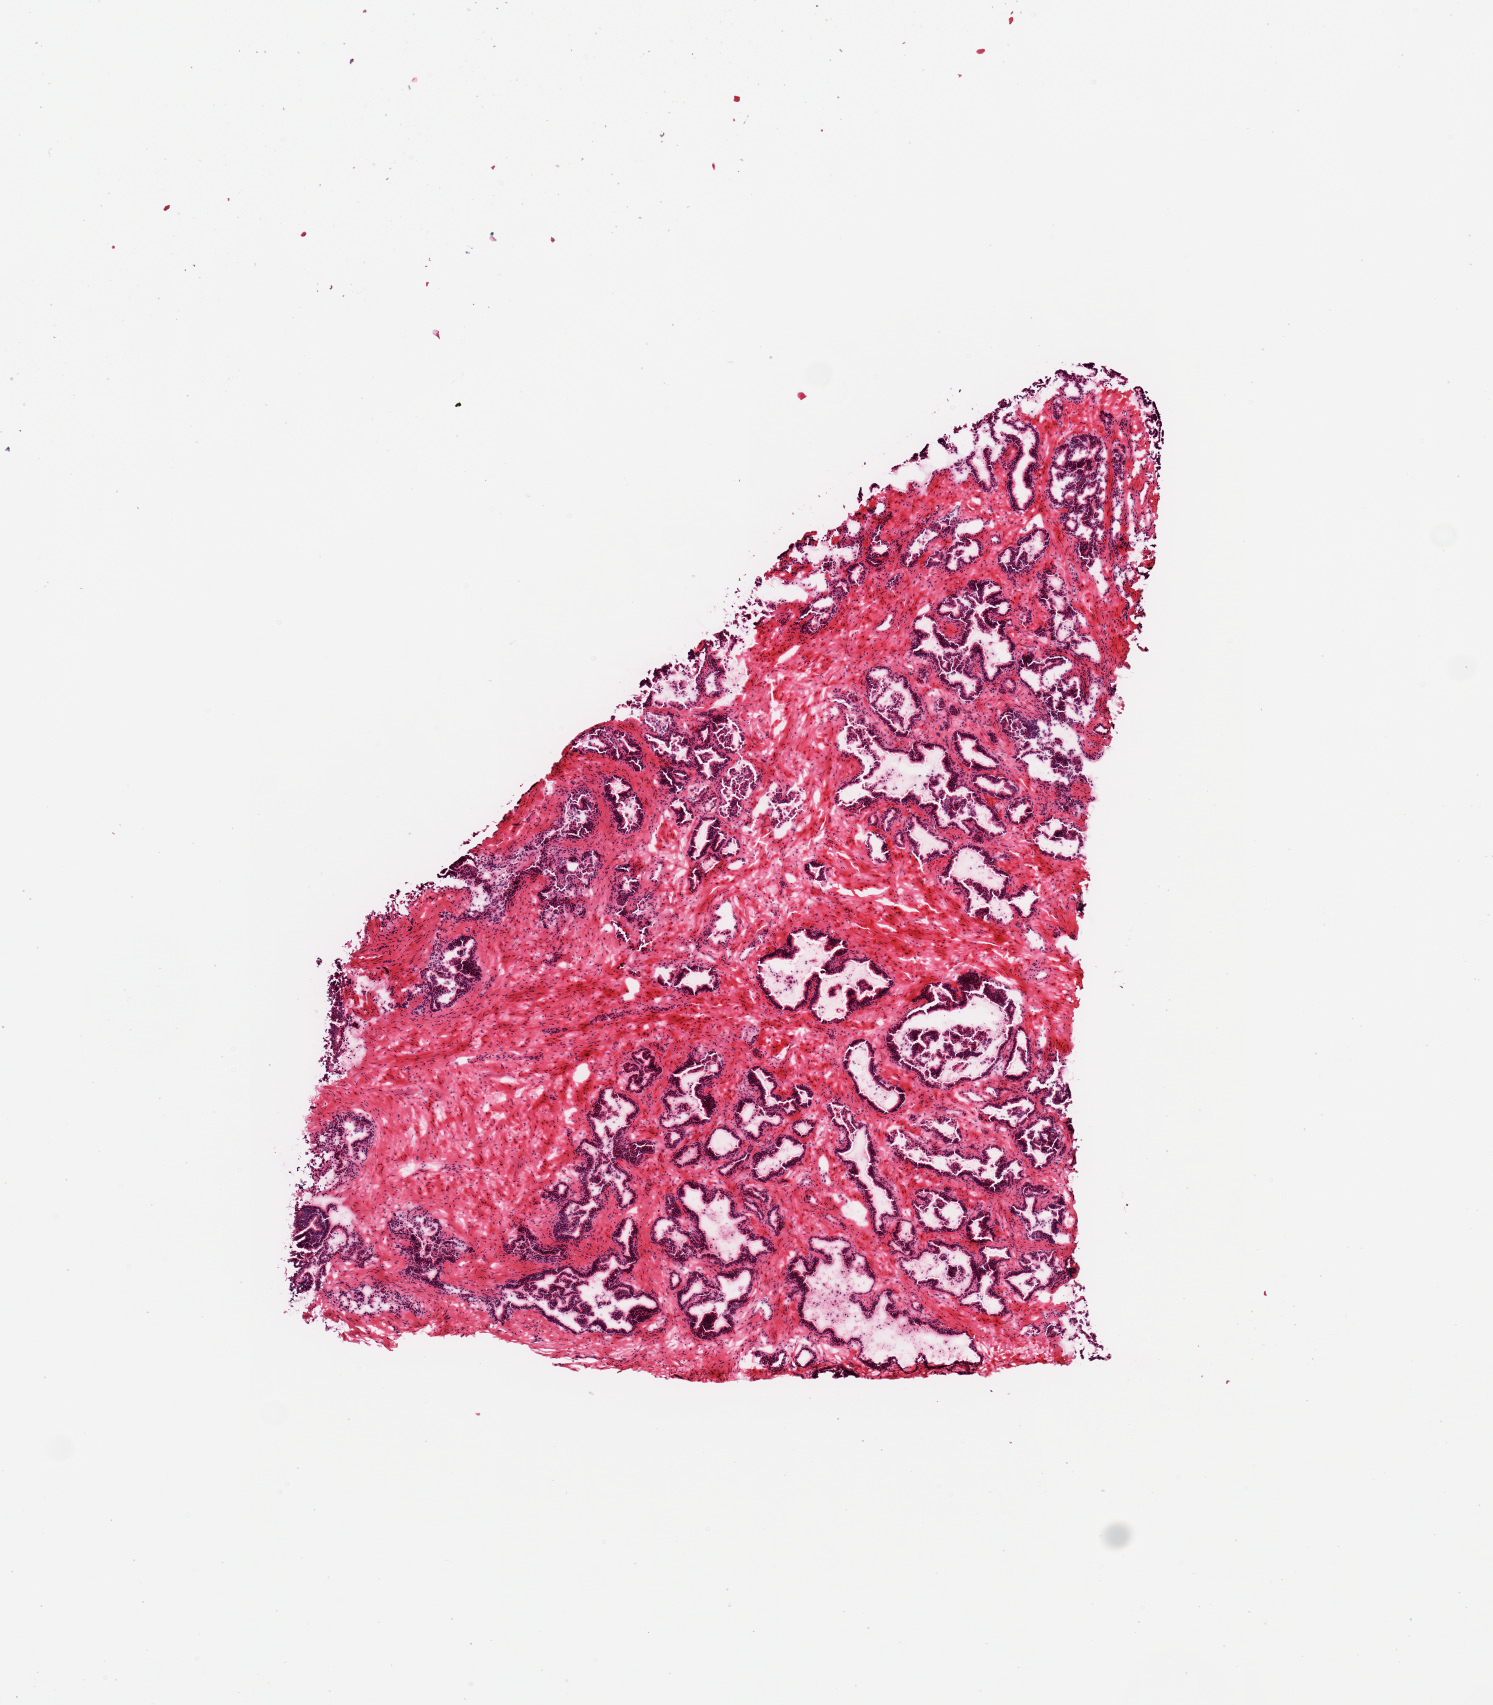
Digitized haematoxylin and eosin-stained section, a low-resolution overview of the entire scanned area, about 5.9 x 6.7 mm. Frozen section (dry ice). Target tissue: prostate. Donor tissue sample. Donor: male.
Reviewer comment on this tissue sample: 1 piece.